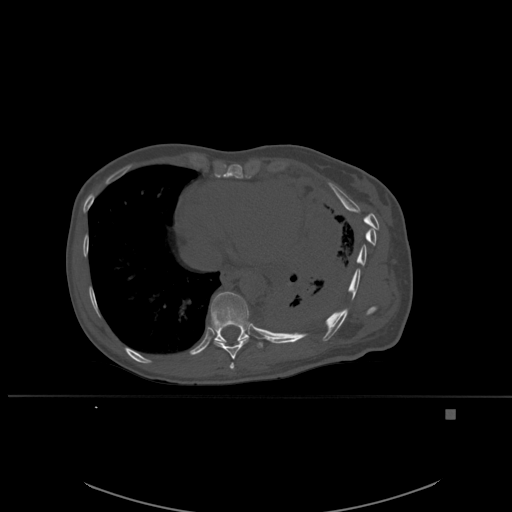
CT including the spine, one axial slice; position 327 of 537 along the scan axis; bone window (W 1800 / L 400 HU); 1.5 mm slice thickness; 512 × 512 image matrix, field of view 440 × 440 mm. Patient: female, 45 years. Case-level facts recorded for this patient, not image findings: primary cancer: lung.
Annotated regions visible in this slice (semi-automatically segmented with operator editing):
- T10 vertebra: bounding box [x1, y1, x2, y2] px = [210, 292, 263, 349]
- T8 vertebra: [229, 362, 234, 370]
- T9 vertebra: [214, 339, 249, 360]